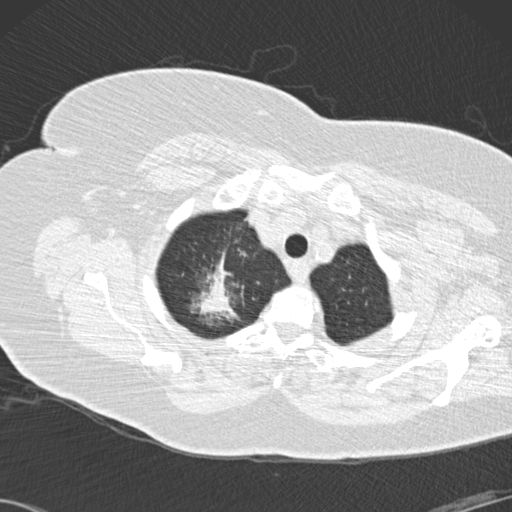
Low-dose screening chest CT, one axial slice. Slice 127 of 146 in the series (ordered by position). 120 kVp. Lung window (W 1500 / L -600 HU). 2 mm slice thickness. 512 × 512 image matrix, field of view 350 × 350 mm.
Outlined on this slice (manually delineated by an expert):
- lesion 1 (tumor, upper lobe of right lung): bounding box <192,253,237,317> (left, top, right, bottom; pixels)